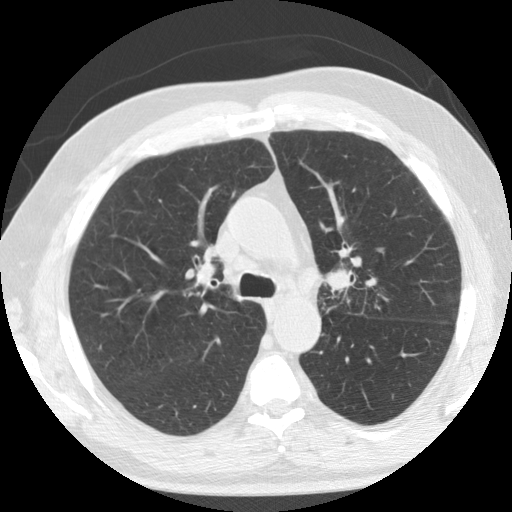
Chest CT (low-dose screening protocol), one axial image; second annual screen; lung window (W 1500 / L -600 HU); 2.5 mm slice thickness; standard (soft-tissue) reconstruction kernel (STANDARD); 120 kVp; slice 45 of 133 in the series; 512 × 512 image matrix. Male participant, aged 74 years at enrolment. Current smoker at enrolment.
Expert reader's lesion annotation, box from (x=303, y=254) to (x=369, y=319) px. No non-calcified nodule or mass ≥4 mm was recorded by the screening reader at this exam. Lung cancer was diagnosed 274 days after this screen: non-small cell carcinoma, left upper lobe, poorly differentiated (G3), stage IIB (AJCC 6th edition).